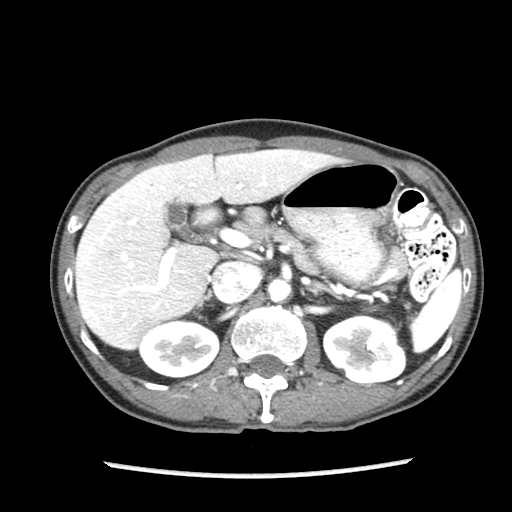
Contrast-enhanced abdominal CT (liver protocol), one axial slice. Position 51 of 87 along the scan axis. Reconstruction kernel STANDARD. 140 kVp. Soft-tissue window (W 400 / L 40 HU). 512 × 512 image matrix. Case-level facts recorded for this patient, not image findings: diagnosis: hepatocellular carcinoma (patient treated with transarterial chemoembolisation; whether this scan precedes or follows treatment is not stated here); TNM stage (as recorded): Stage-IIIB; Child-Pugh class: A; tumour differentiation: well differentiated; tumour nodularity: uninodular.
Outlined on this slice (semi-automatically segmented with operator editing):
- liver parenchyma outside the tumour (the mass and vessels are separate outlines, so this box may not span the whole liver): bounding box [x1, y1, x2, y2] px = [76, 148, 343, 349]
- liver vessels: [83, 152, 307, 316]